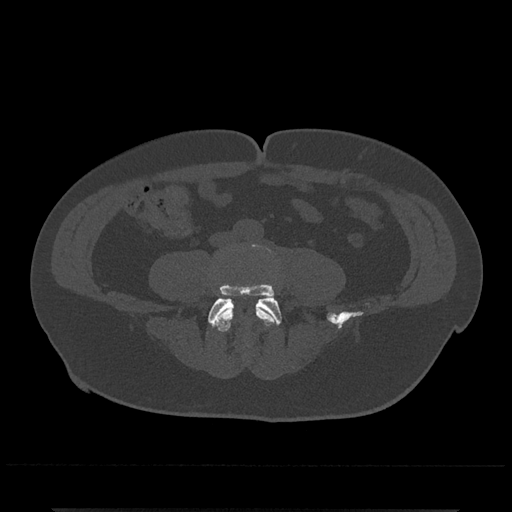
CT including the spine, one axial slice. Slice 115 of 797 in the series (ordered by position). Reconstruction kernel Br40s/3. Bone window (W 1800 / L 400 HU). 512 × 512 image matrix, field of view 393 × 393 mm. Male patient, age 67 years. Case-level facts recorded for this patient, not image findings: primary cancer: prostate.
Structures marked on this image (semi-automatic segmentation, software-assisted and operator-edited):
- L4 vertebra: bounding box <211,301,278,332> (left, top, right, bottom; pixels)
- L5 vertebra: <208,244,282,326>